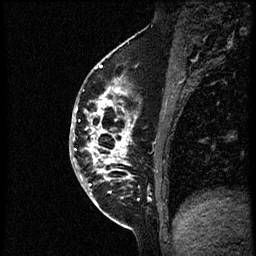
Breast MRI (dynamic contrast-enhanced), one sagittal slice. Slice 26 of 56 in the series (ordered by position). Dynamic contrast-enhanced study with each time point stored as its own series, time point 2 of 3 at this slice position (early post-contrast, ordered by acquisition time). 1.5 T. TE 4.2 ms, TR 21.3 ms. 2 mm slice thickness. 256 × 256 image matrix, field of view 200 × 200 mm. Patient: female, 41 years. Case-level facts recorded for this patient, not image findings: setting: breast cancer imaged before/during neoadjuvant chemotherapy; receptor status: HER2-positive.
Annotated regions visible in this slice (semi-automatic segmentation, software-assisted and operator-edited):
- analysis volume of interest (the breast-tissue region the enhancement analysis was run in; not a lesion): bounding box [x1, y1, x2, y2] px = [70, 73, 177, 205]
- tumour enhancement mask (voxels above the 100 % enhancement threshold inside the analysis volume of interest): [74, 78, 150, 205]